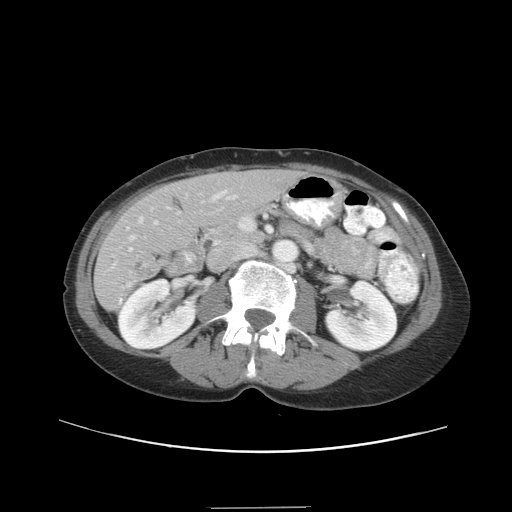
Contrast-enhanced abdominal CT, one axial slice; reconstruction kernel STANDARD; 120 kVp; soft-tissue window (W 400 / L 40 HU); 512 × 512 image matrix, field of view 388 × 388 mm. Female patient, age 64 years. Case-level facts recorded for this patient, not image findings: diagnosis: colorectal cancer liver metastases, imaged before liver resection; multiple liver metastases: no; largest metastasis: 3.8 cm; disease in both lobes: yes.
Annotated regions visible in this slice (manually delineated by an expert):
- hepatic veins: bounding box (x1, y1, x2, y2) in pixels: (129, 195, 237, 240)
- liver: (96, 172, 297, 310)
- planned liver remnant (the part of the liver to remain after resection): (144, 172, 297, 236)
- portal vein (with intrahepatic branches): (126, 190, 227, 251)